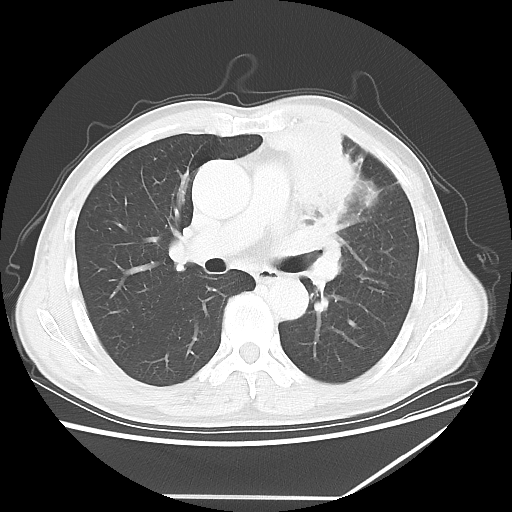
Chest CT, one axial slice; position 36 of 64 along the scan axis; reconstruction kernel LUNG; 100 kVp; lung window (W 1500 / L -600 HU); 5 mm slice thickness; 512 × 512 image matrix, field of view 383 × 383 mm. Patient: male, 64 years. Case-level facts recorded for this patient, not image findings: clinical TNM (as recorded): T1c N1 M1; histopathological grade: G2.
Outlined on this slice (bounding box drawn by a radiologist):
- lung tumour (recorded histology: squamous cell carcinoma): box from (x=248, y=112) to (x=392, y=231) px